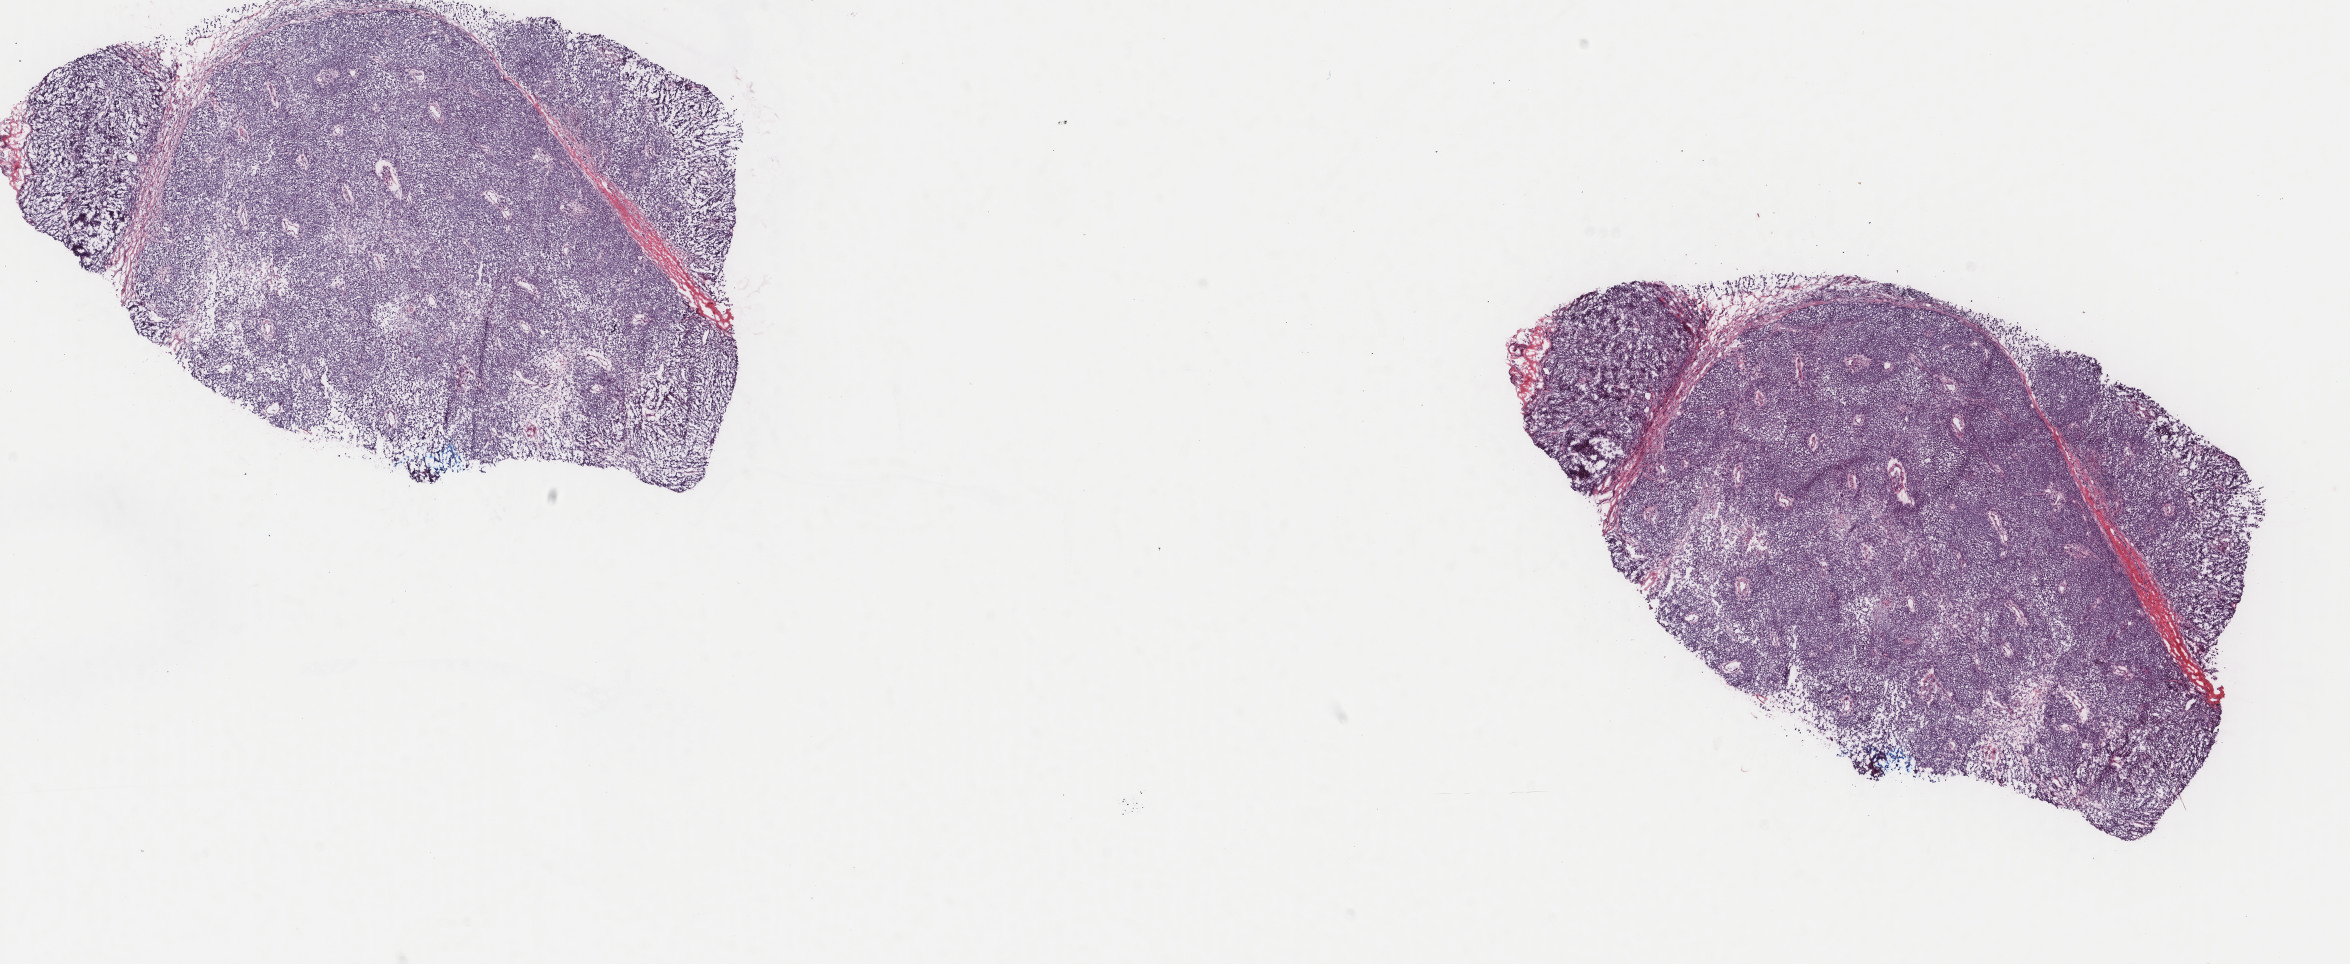
Whole-slide histology image, H&E, whole scanned area (about 18.7 x 7.7 mm, from a 40x scan) shown as a low-resolution overview. Frozen section from the top of the tissue portion. Skin, primary tumour sample. Male, age 54 years at initial diagnosis. Composition of this section per pathologist review: tumour cells 100%, tumour nuclei 90%, normal cells 0%, stromal cells 0%, necrosis 0%. Inflammatory infiltration, as recorded: lymphocyte infiltration 3%, monocyte infiltration 0%, neutrophil infiltration 0%.
* AJCC pathologic stage: IIIC (7th edition)
* histologic diagnosis: Malignant melanoma, NOS